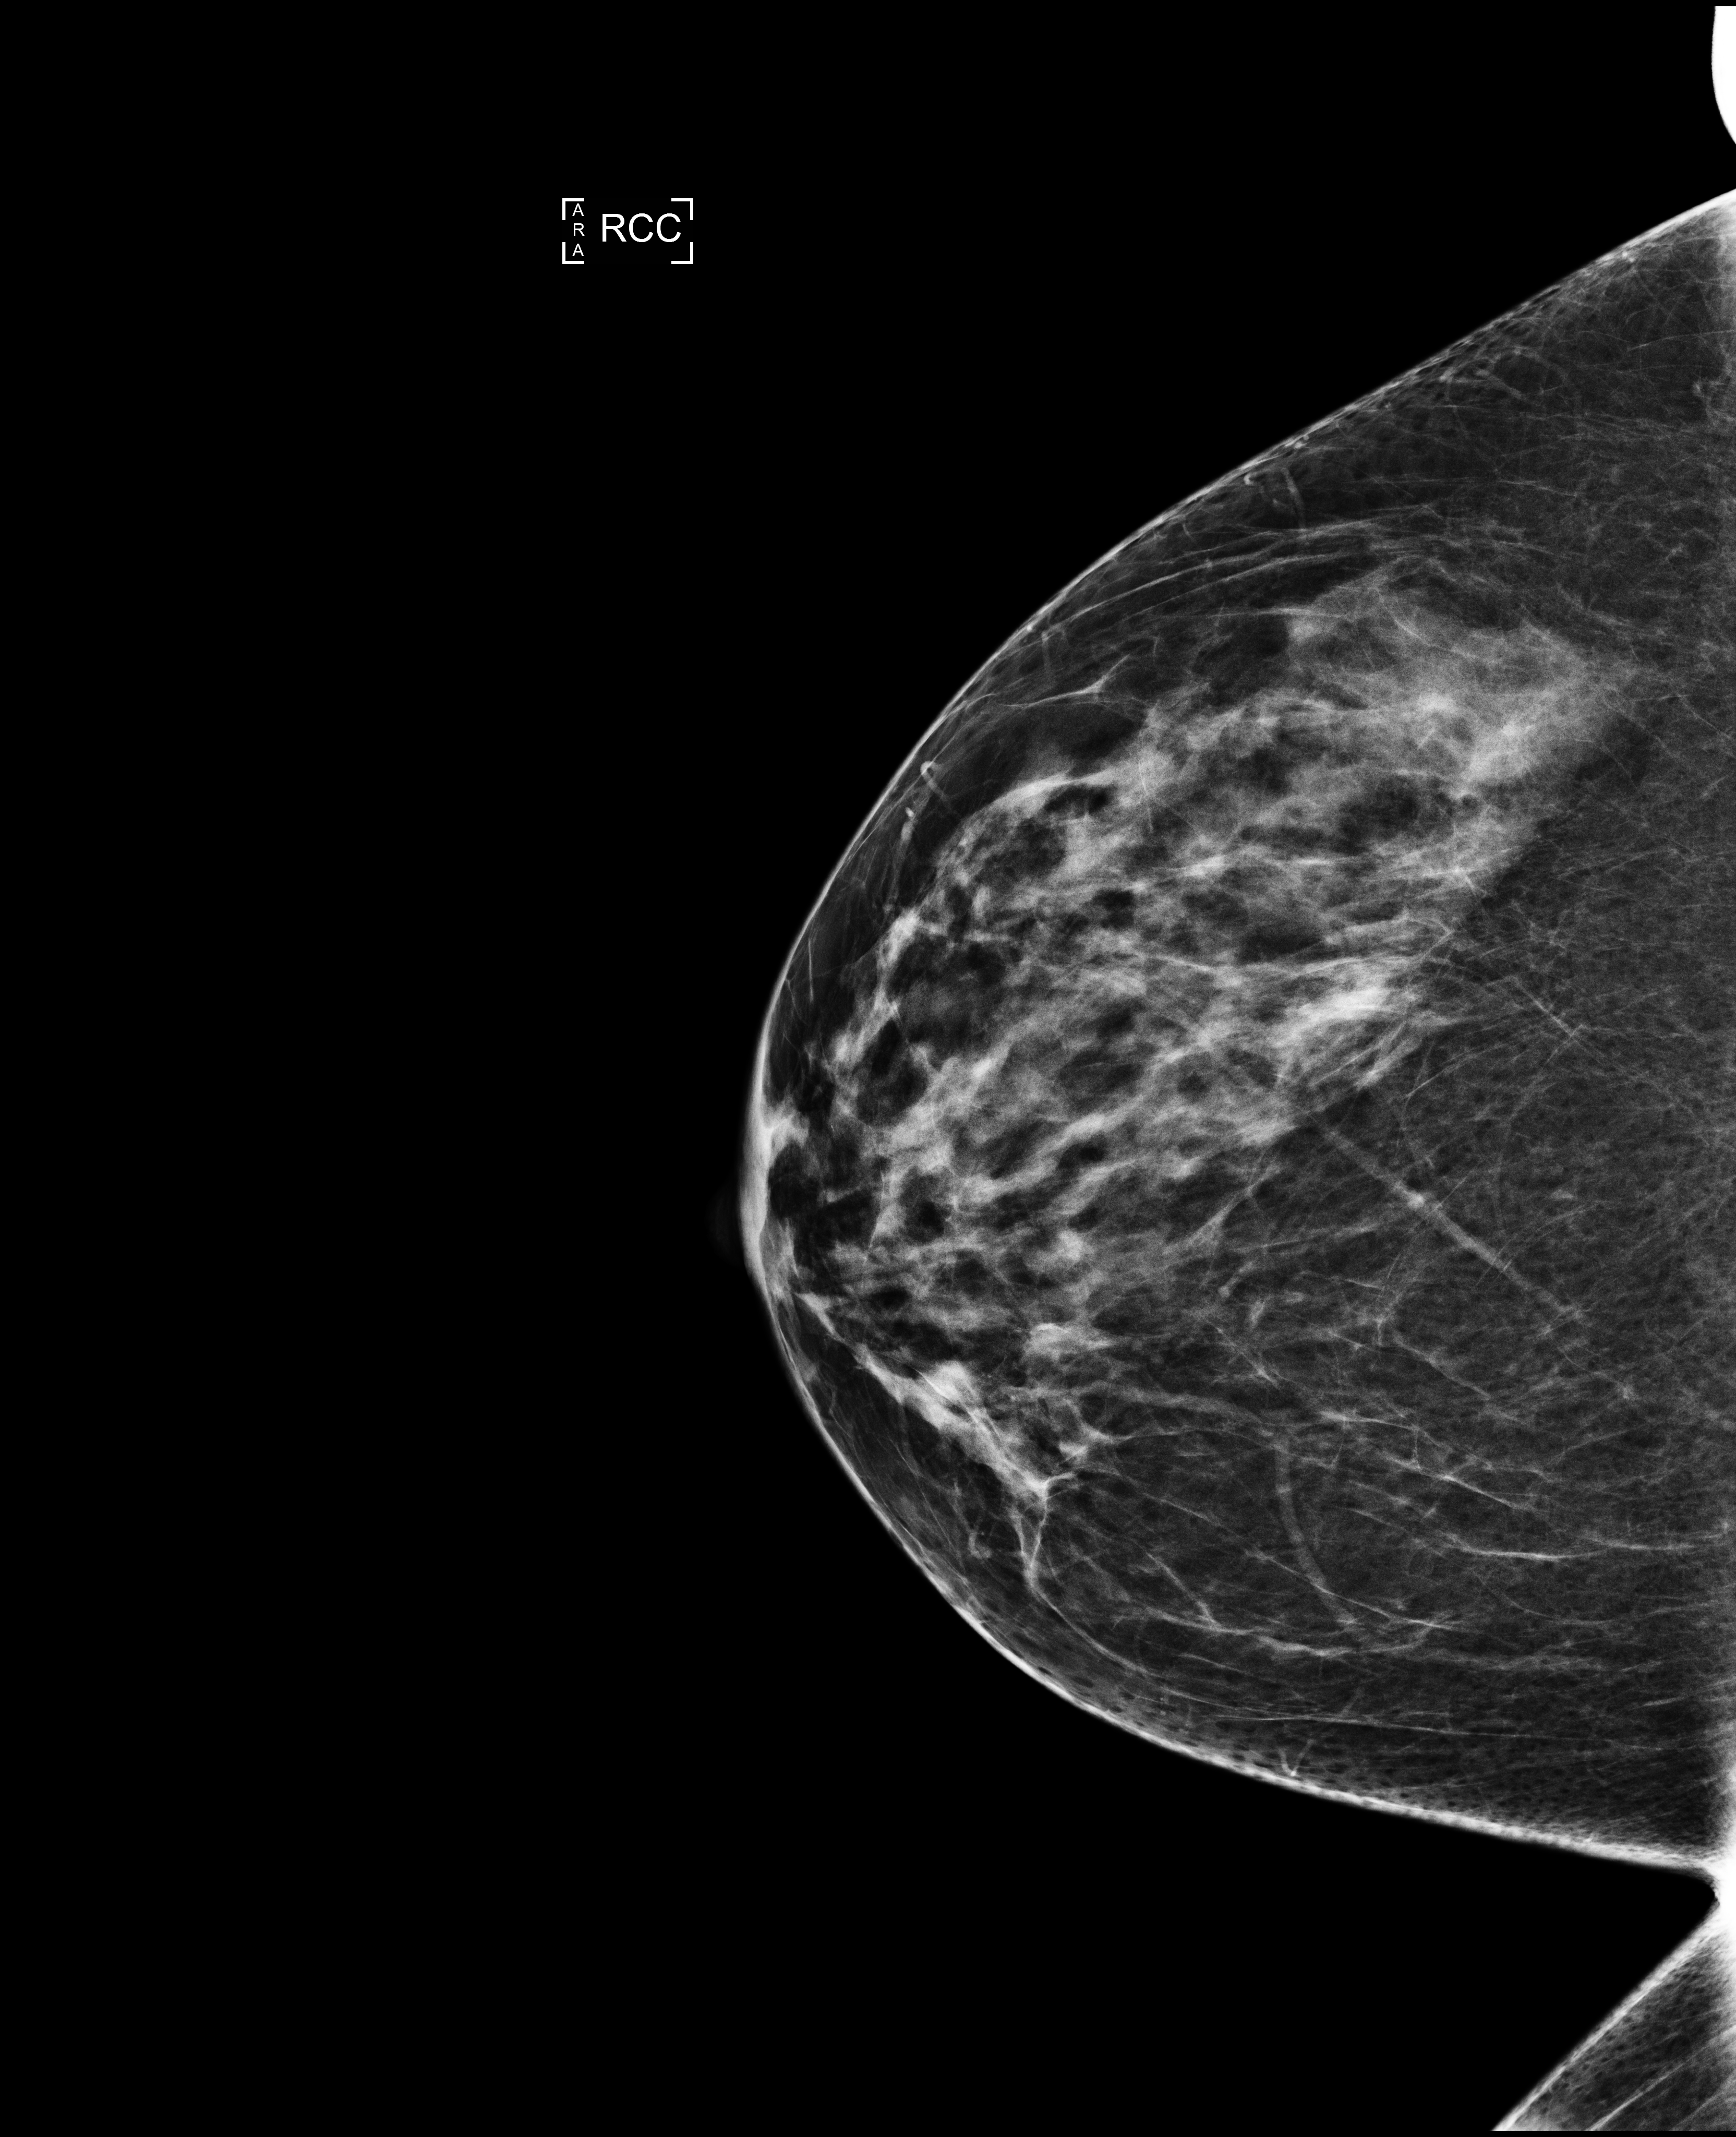
Digital mammogram (FFDM), right breast, CC view, screening examination, compressed breast thickness 57 mm, system: Selenia Dimensions. Patient: female, 51 years.
Breast density at the screening exam (both breasts): heterogeneously dense (BI-RADS density category c). Final BI-RADS assessment for this screening round (tomosynthesis exam, both breasts): category 1. Recall: no recall after this screen.